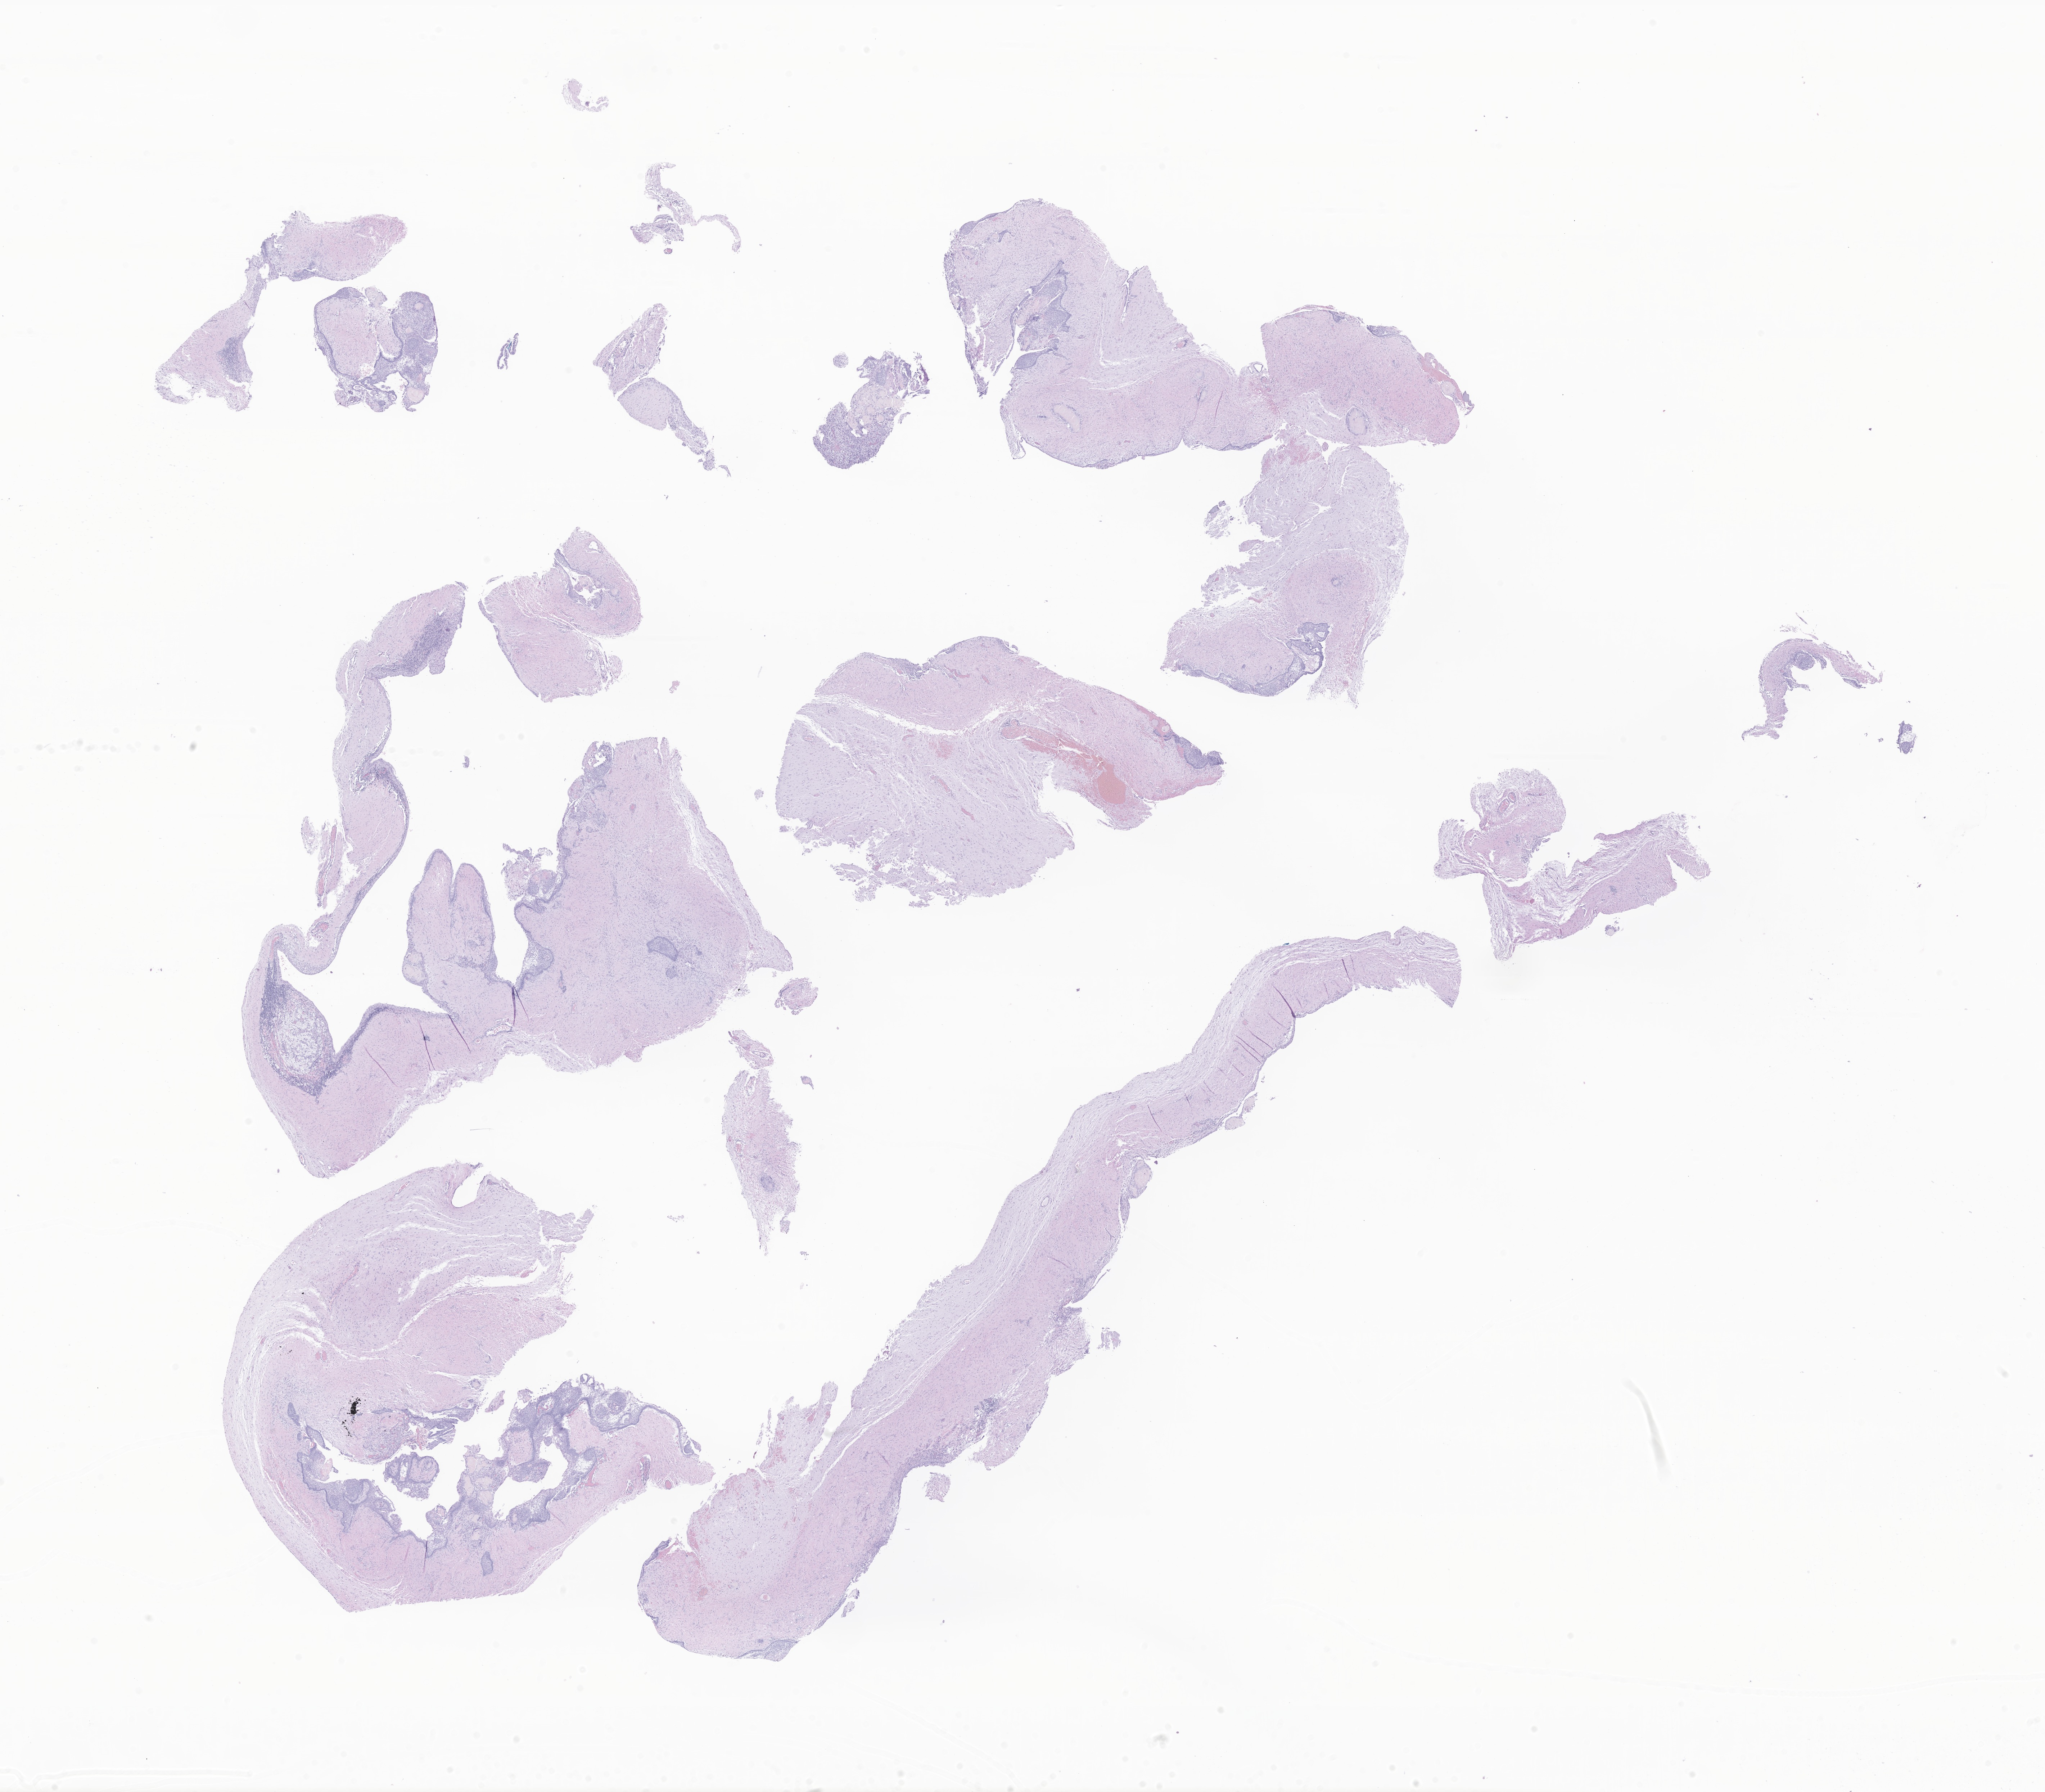
H&E whole-slide image of tumor tissue from the brain, shown as a low-resolution overview of the whole scanned area (about 24.0 x 21.0 mm), FFPE section. Male patient, age 161 months (13 years 5 months).
Diagnosis (ICD-O-3 morphology term): Craniopharyngioma, adamantinomatous.